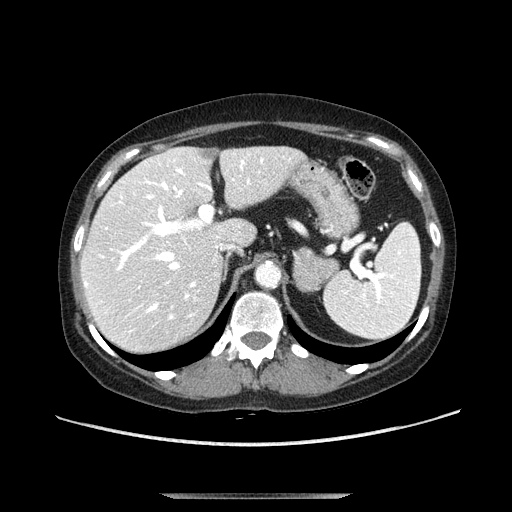
Contrast-enhanced abdominal CT, one axial slice; slice 74 of 107 in the series (ordered by position); soft-tissue window (W 400 / L 40 HU); 512 × 512 image matrix. Female patient. From the clinical record (not read from this slice): diagnosis: adrenocortical carcinoma; tumour side: left adrenal; tumour size at pathology: 7.5 cm; Ki-67 index: 9 %; stage (as recorded): 3.
Outlined on this slice (semi-automatically segmented with operator editing):
- mass: bounding box (x1, y1, x2, y2) in pixels: (293, 246, 340, 293)